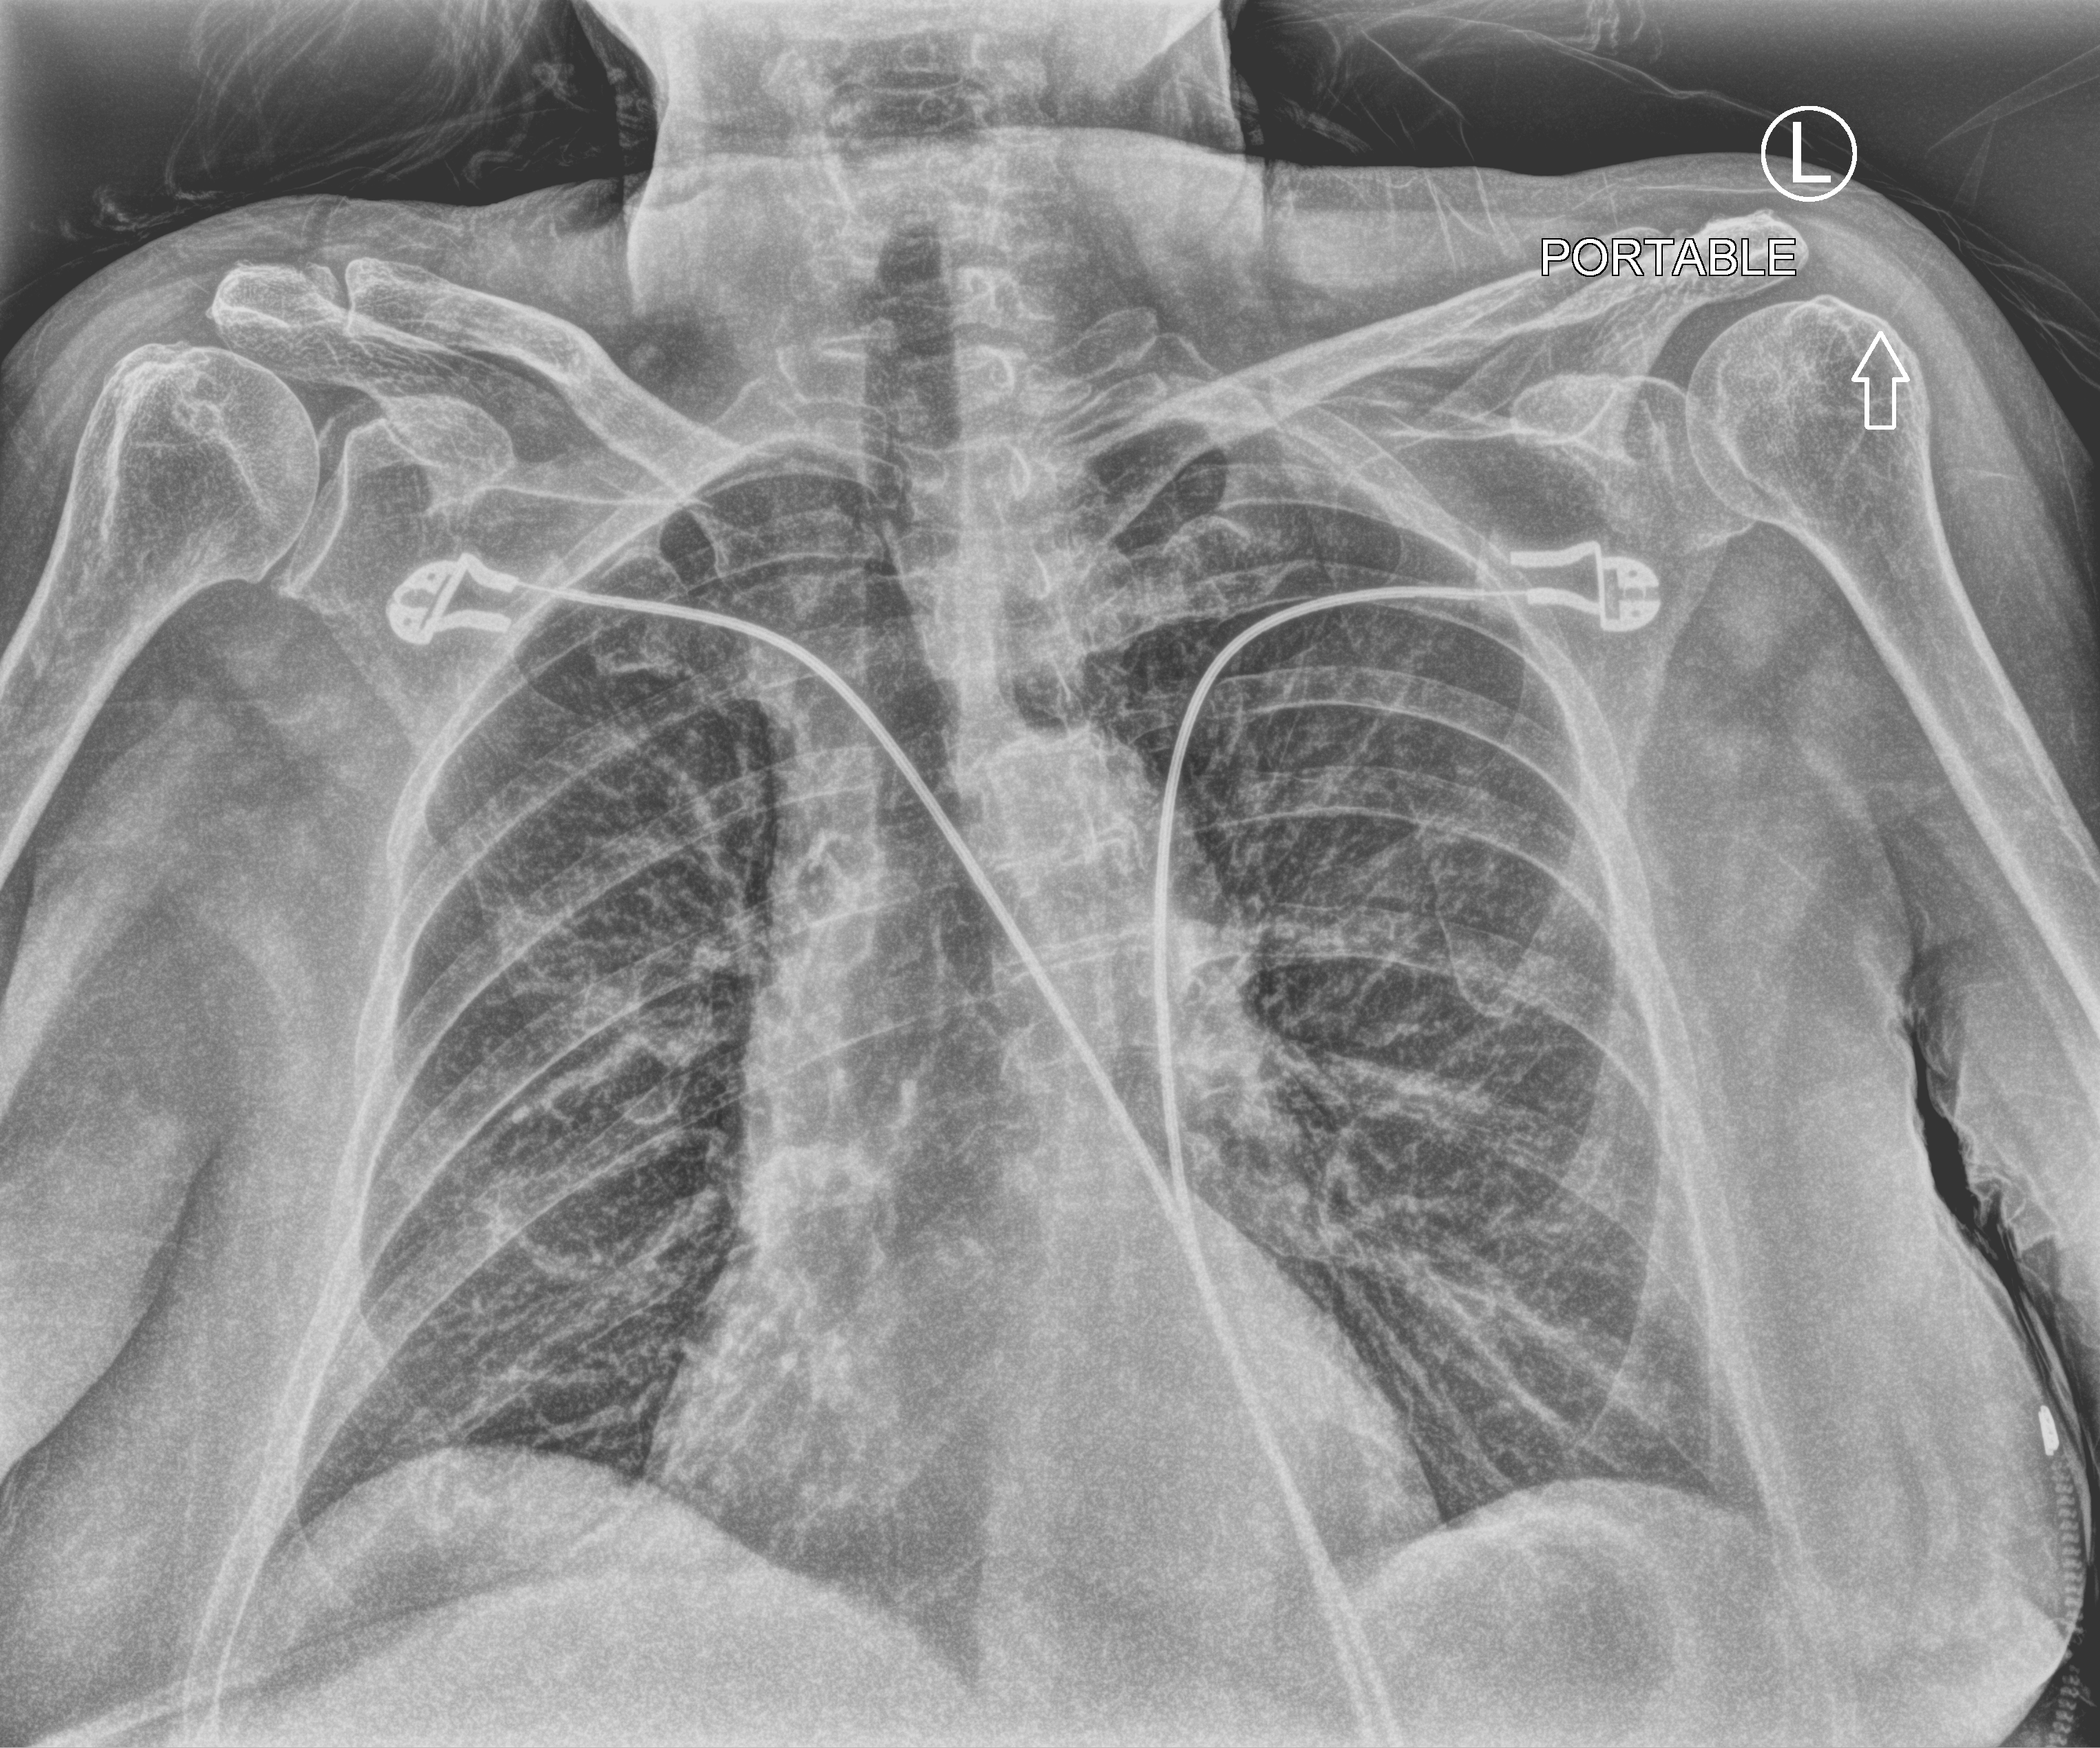
Chest X-ray (portable); anteroposterior (AP) projection. Female patient hospitalised with COVID-19, age 75–90 years.
Admission-level facts for this patient (not findings on this image; timing relative to this image not recorded):
- length of hospital stay: 6 days
- mechanically ventilated during this hospital stay: no